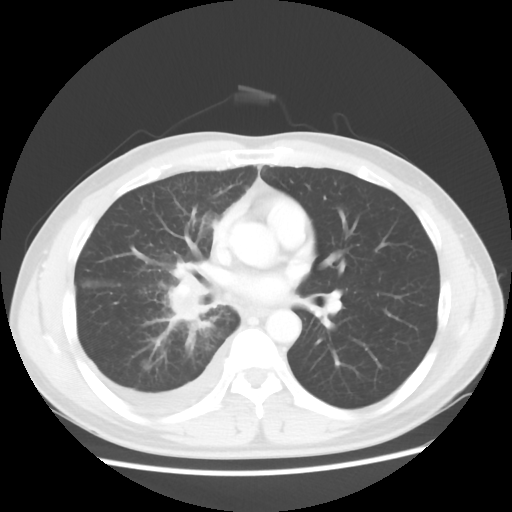
Chest CT, one axial slice; slice 28 of 56 in the series (ordered by position); reconstruction kernel STANDARD; 120 kVp; lung window (W 1500 / L -600 HU); 5 mm slice thickness; 512 × 512 image matrix. Patient: male, 46 years. From the clinical record (not read from this slice): clinical TNM (as recorded): T2 N3 M1.
Structures marked on this image (rectangle marked by the reading radiologist):
- lung tumour (recorded histology: adenocarcinoma): bounding box (x1, y1, x2, y2) in pixels: (163, 273, 215, 330)